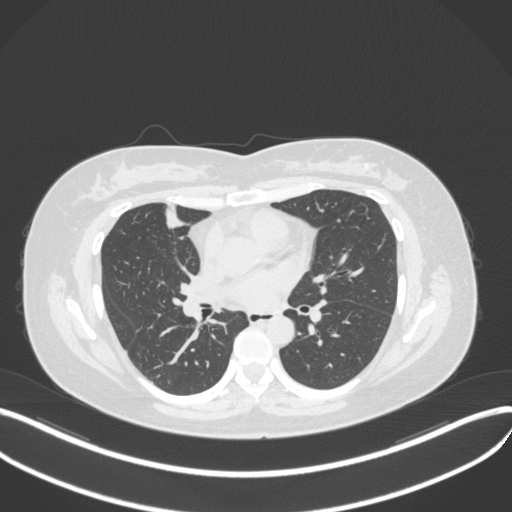
Chest CT, one axial slice; position 163 of 272 along the scan axis; reconstruction kernel B31f; 120 kVp; lung window (W 1500 / L -600 HU); 512 × 512 image matrix, field of view 400 × 400 mm. Female patient, age 42 years. Case-level facts recorded for this patient, not image findings: clinical TNM (as recorded): T1b N0 M0.
Outlined on this slice (rectangle marked by the reading radiologist):
- lung tumour (recorded histology: adenocarcinoma): bounding box <158,198,193,233> (left, top, right, bottom; pixels)